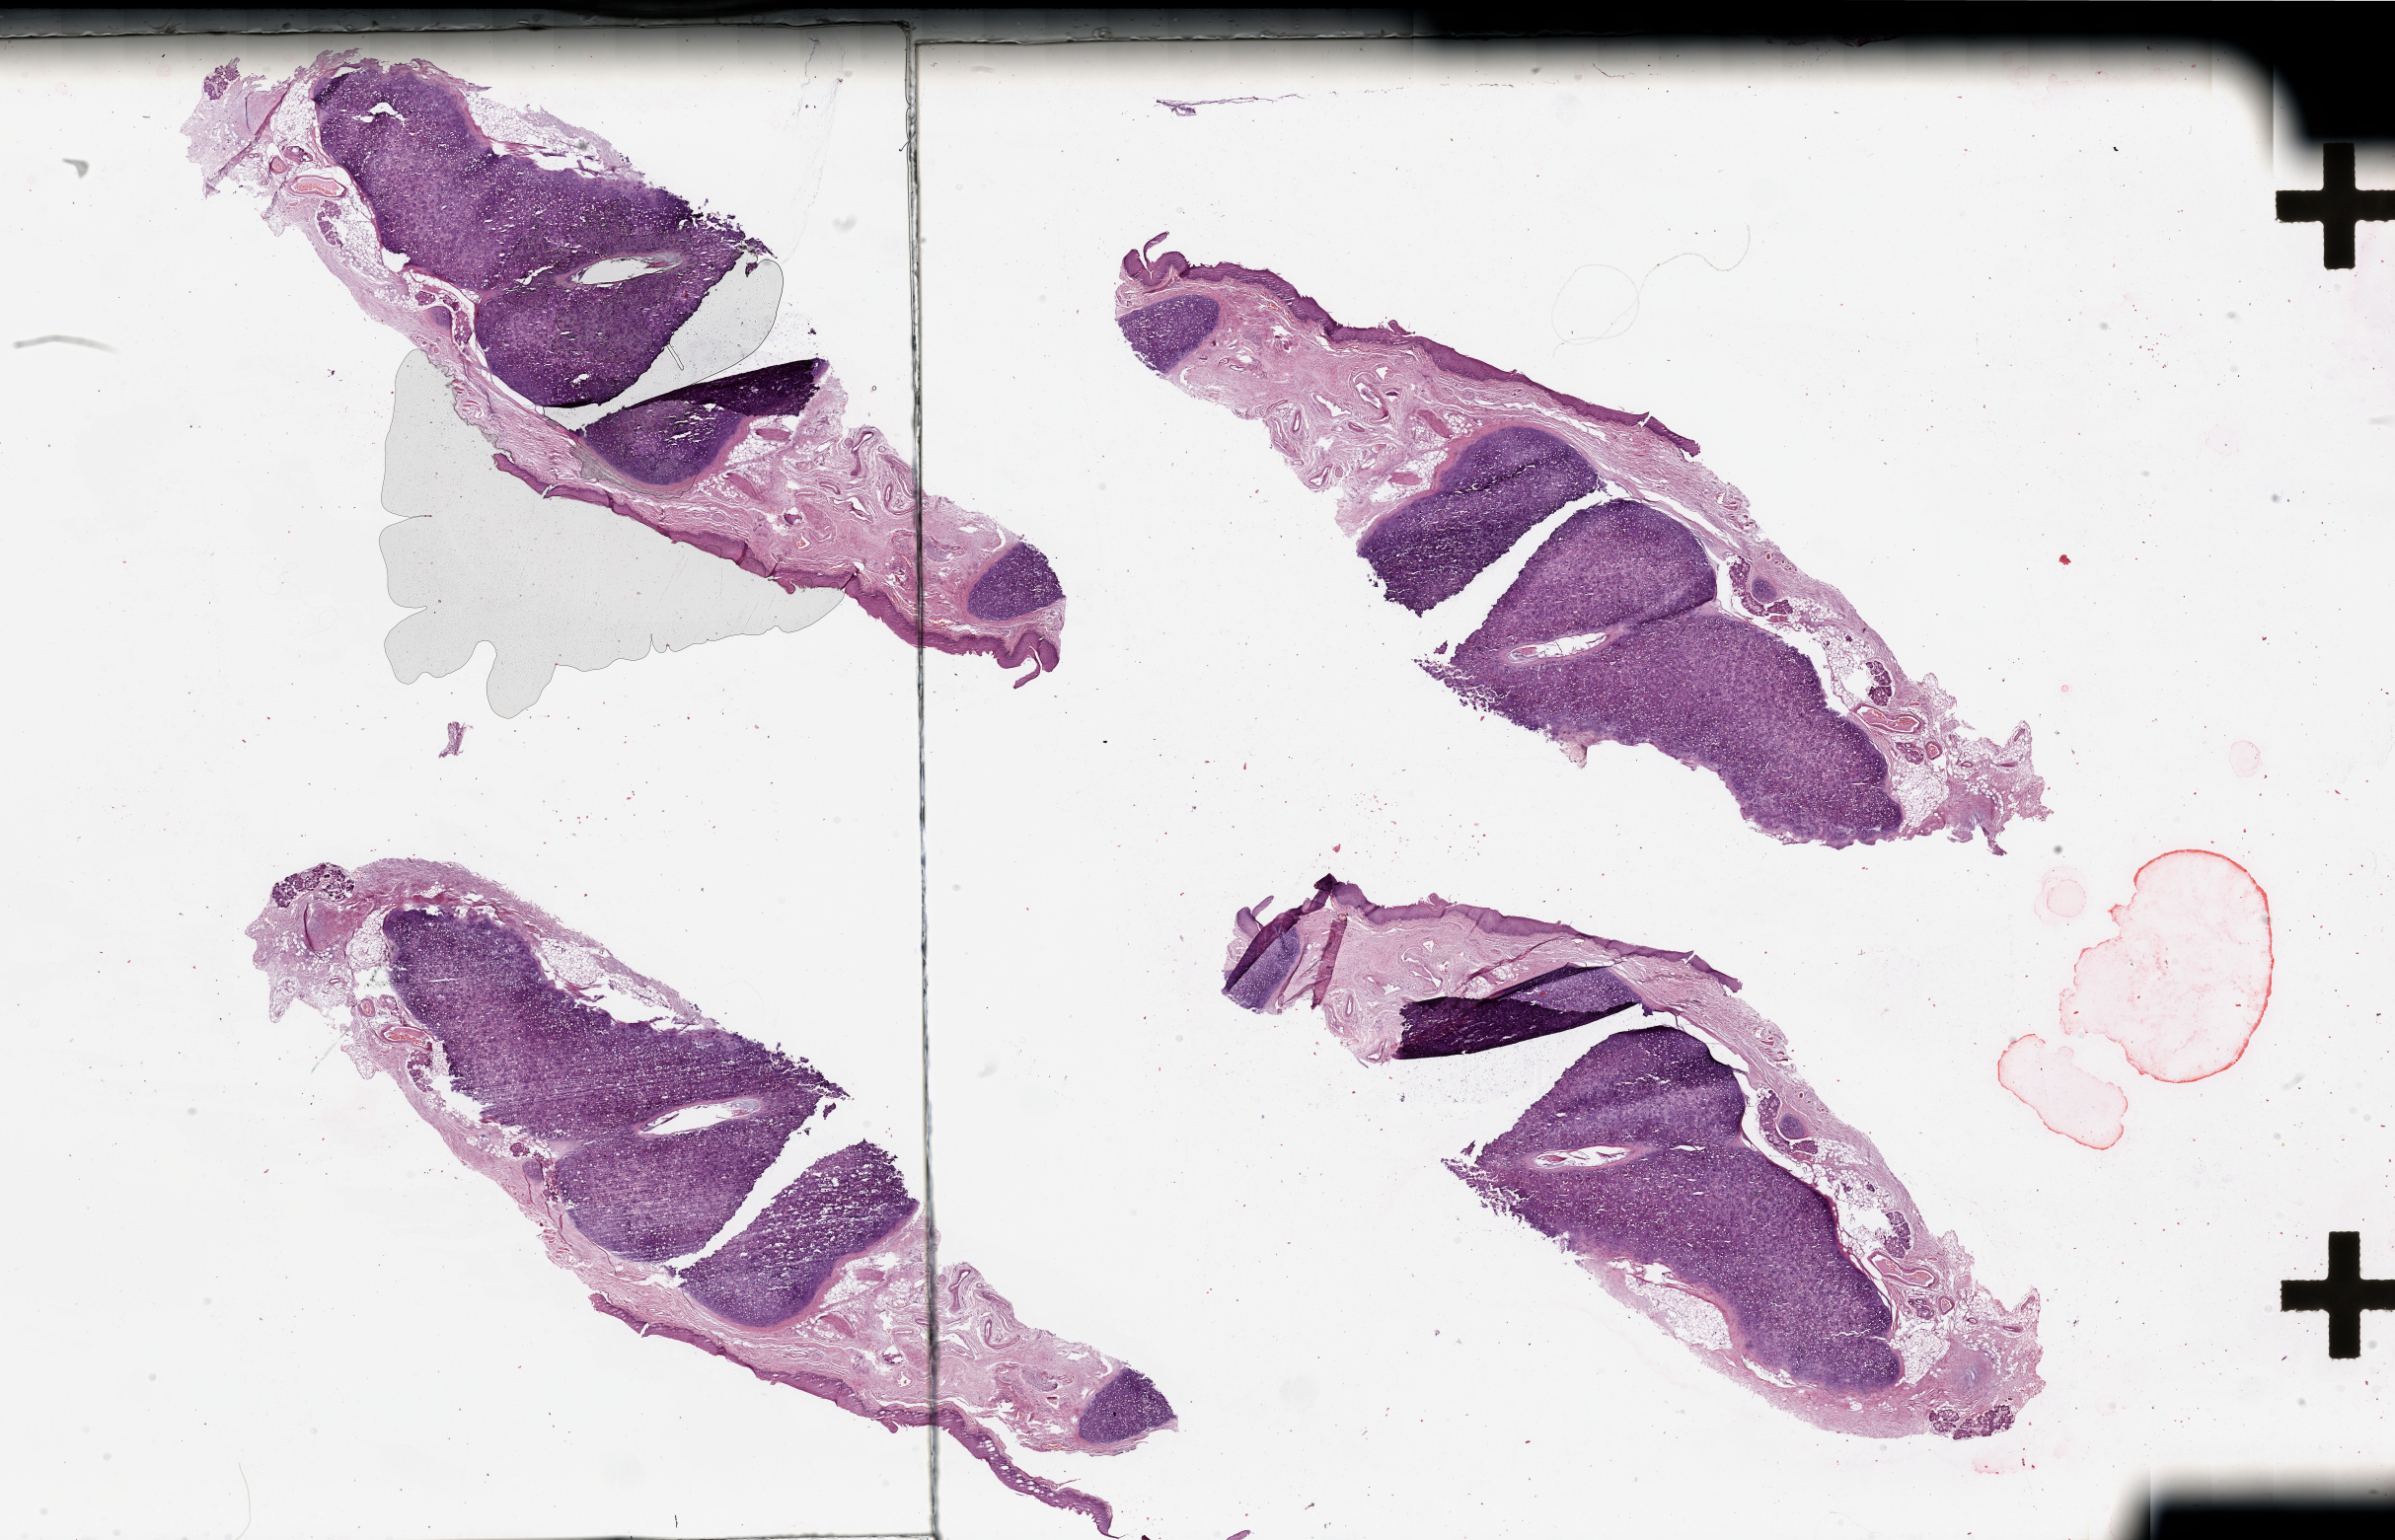
Digitized H&E-stained tissue section (whole slide), whole scanned area (about 38.4 x 24.7 mm, slide scanned at 20x) shown as a low-resolution overview. Normal (non-tumour) tissue sample, sampled site: larynx. 61-year-old male patient.
This section: normal (non-tumour) tissue from the same patient. Patient diagnosis: Squamous cell carcinoma, NOS (larynx, NOS).